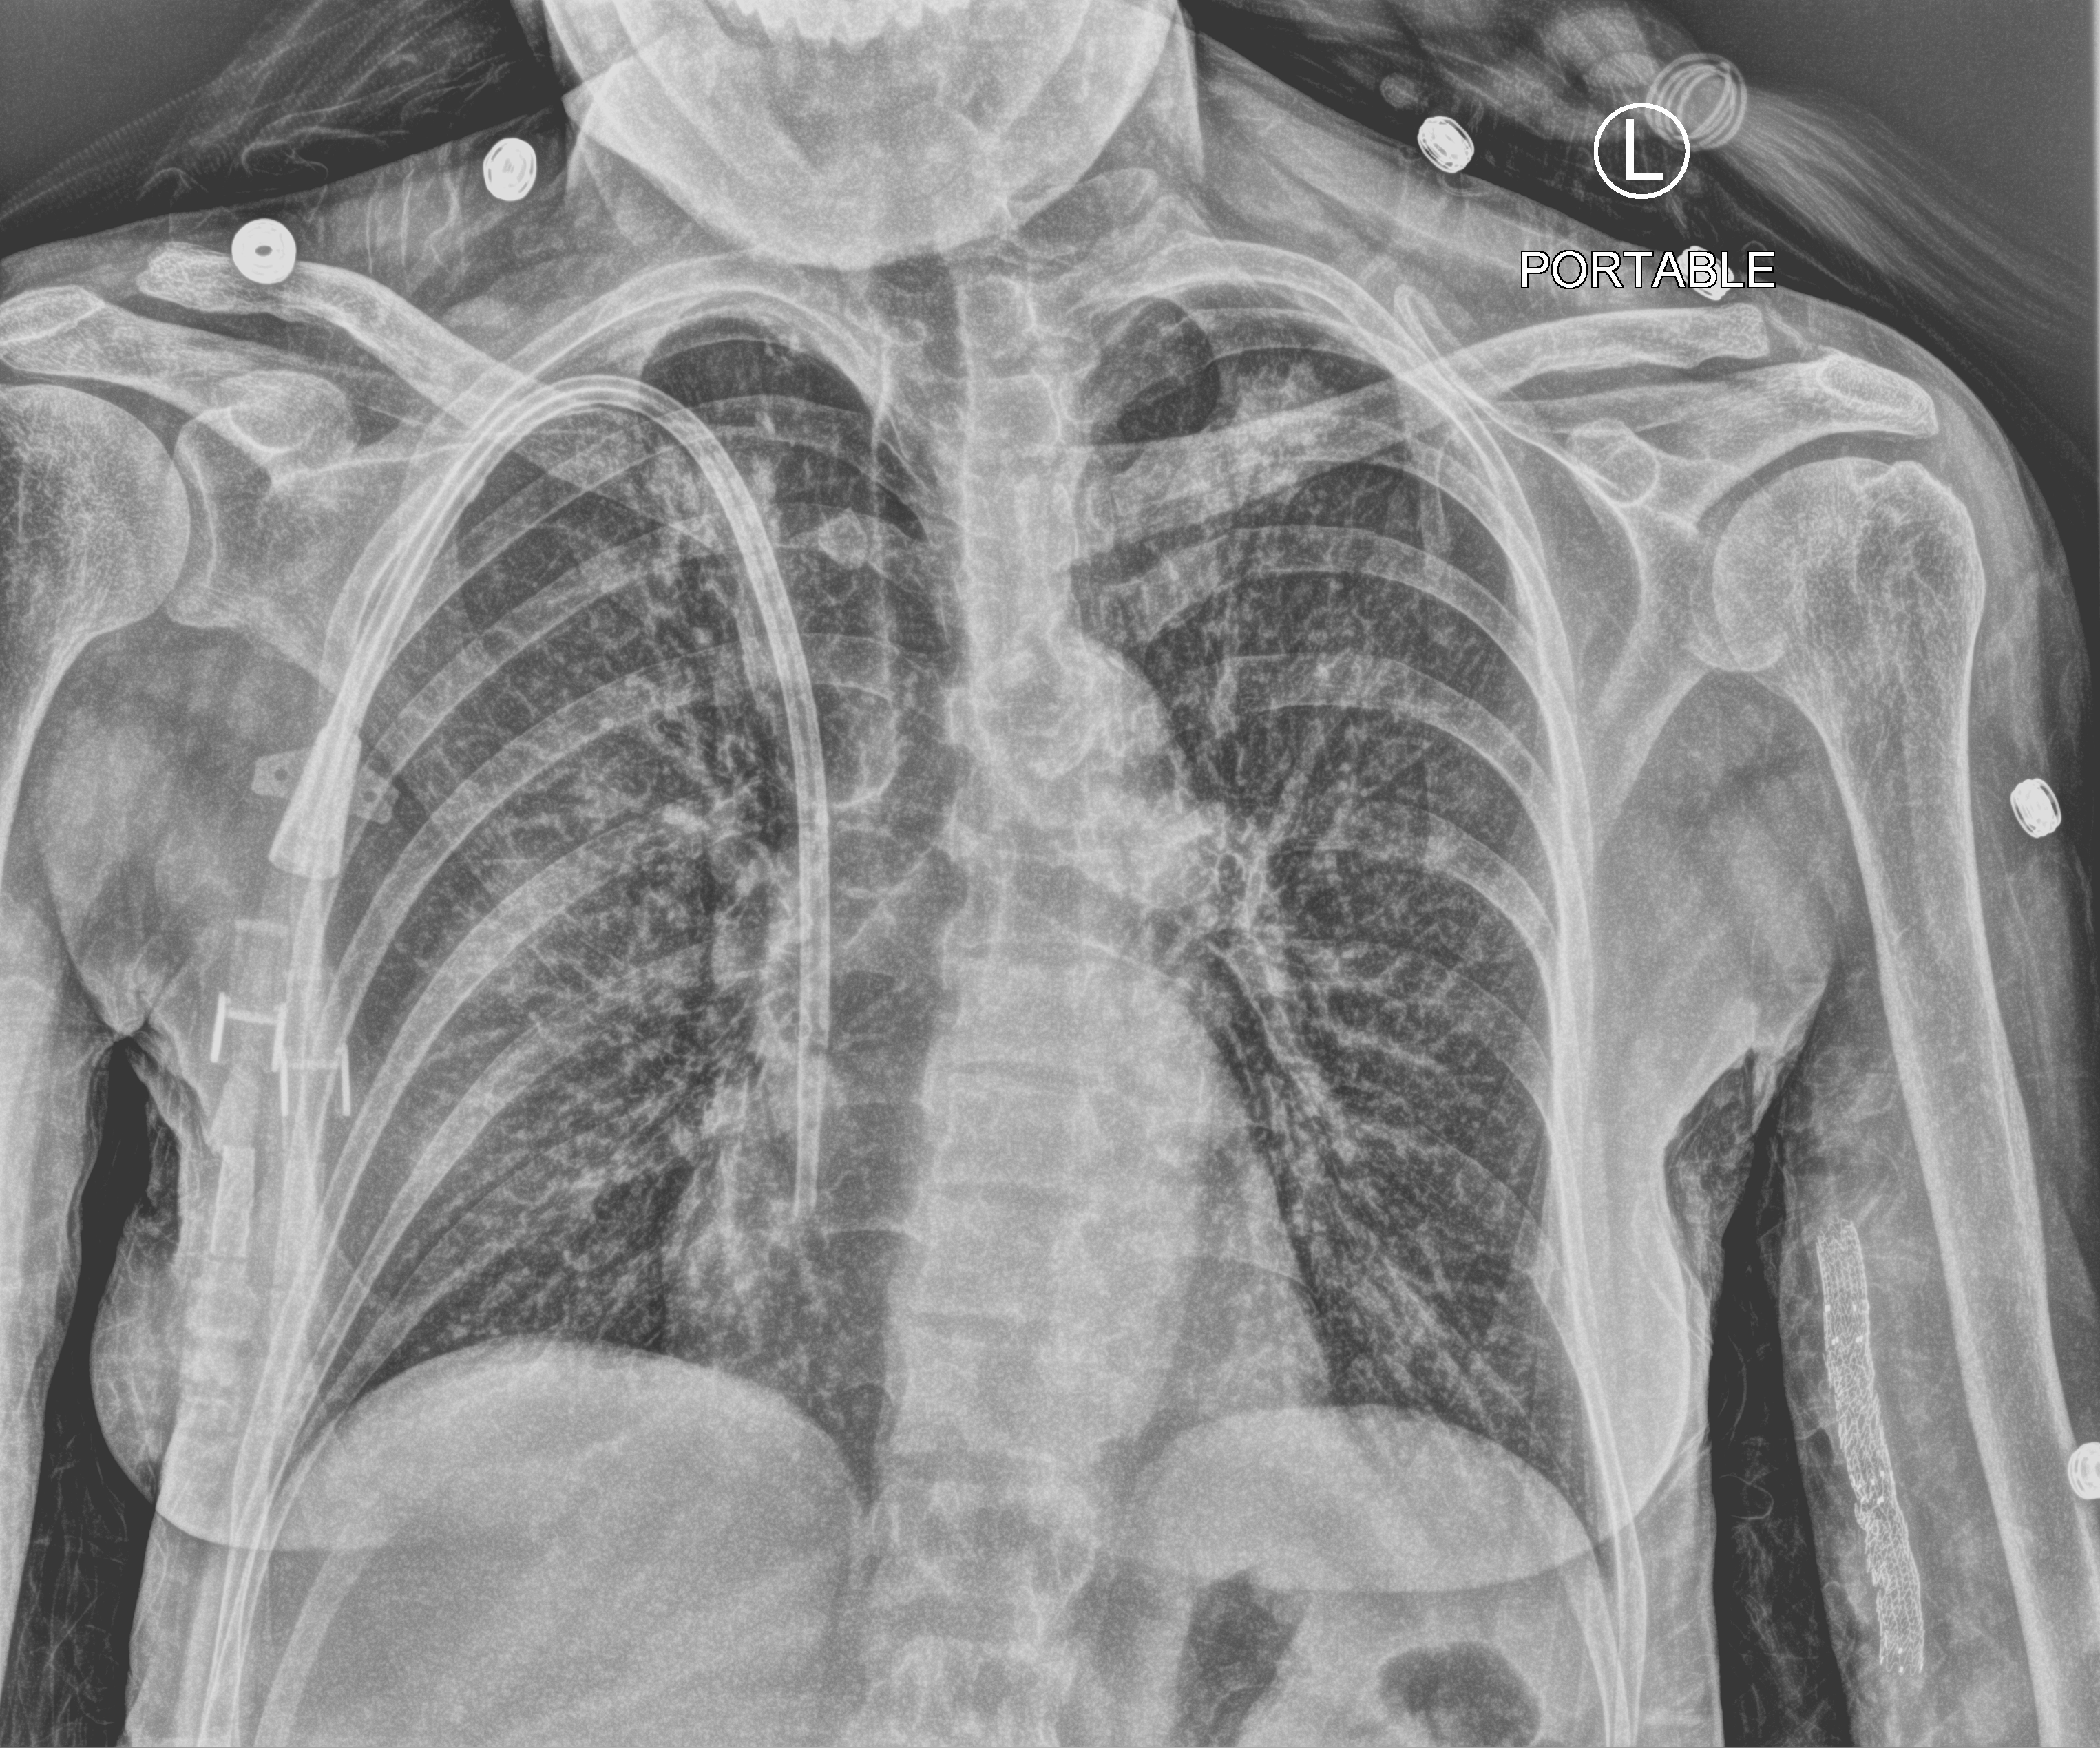
Bedside chest radiograph (computed radiography); anteroposterior (AP) projection. Female patient hospitalised with COVID-19, age 18–59 years.
Hospital-stay facts (about this admission, not read from this image; timing relative to this image not recorded):
- mechanically ventilated during this hospital stay: no
- length of hospital stay: 7 days